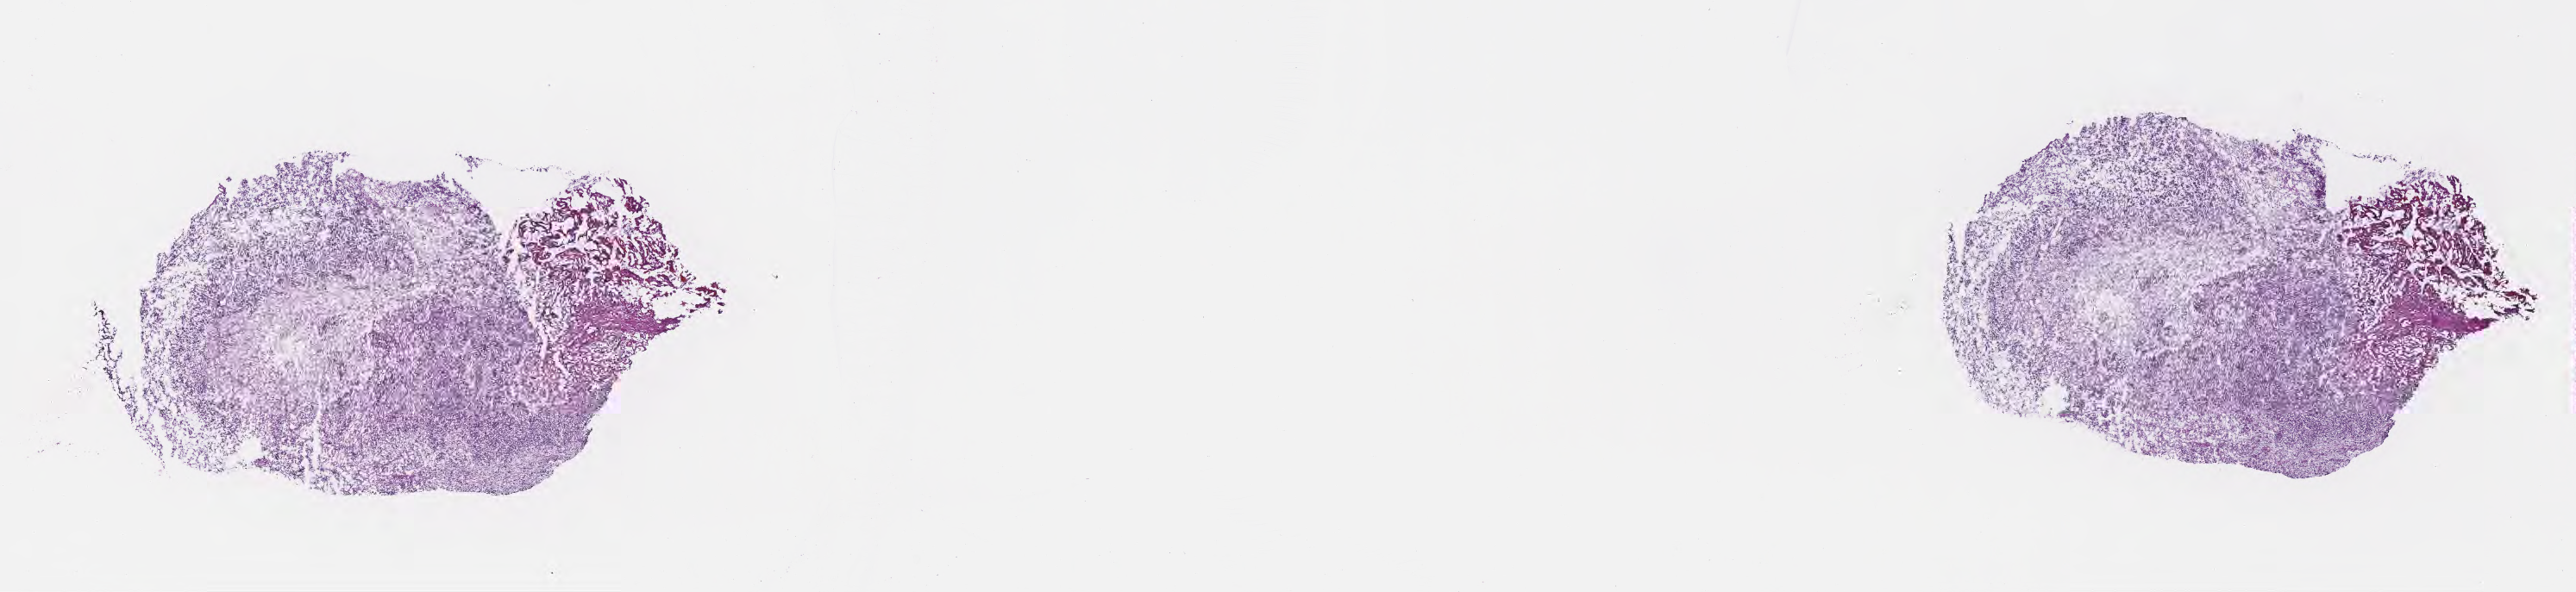
Whole-slide image, H&E stain — low-resolution overview of the scanned area, about 24.2 x 5.6 mm; cryosection; specimen: primary tumor; site: brain. Patient: male, age at initial diagnosis 51 years. Slide review estimates, as recorded: tumor cells 80%, tumor nuclei 91%.
Diagnosis: Glioblastoma, NOS.